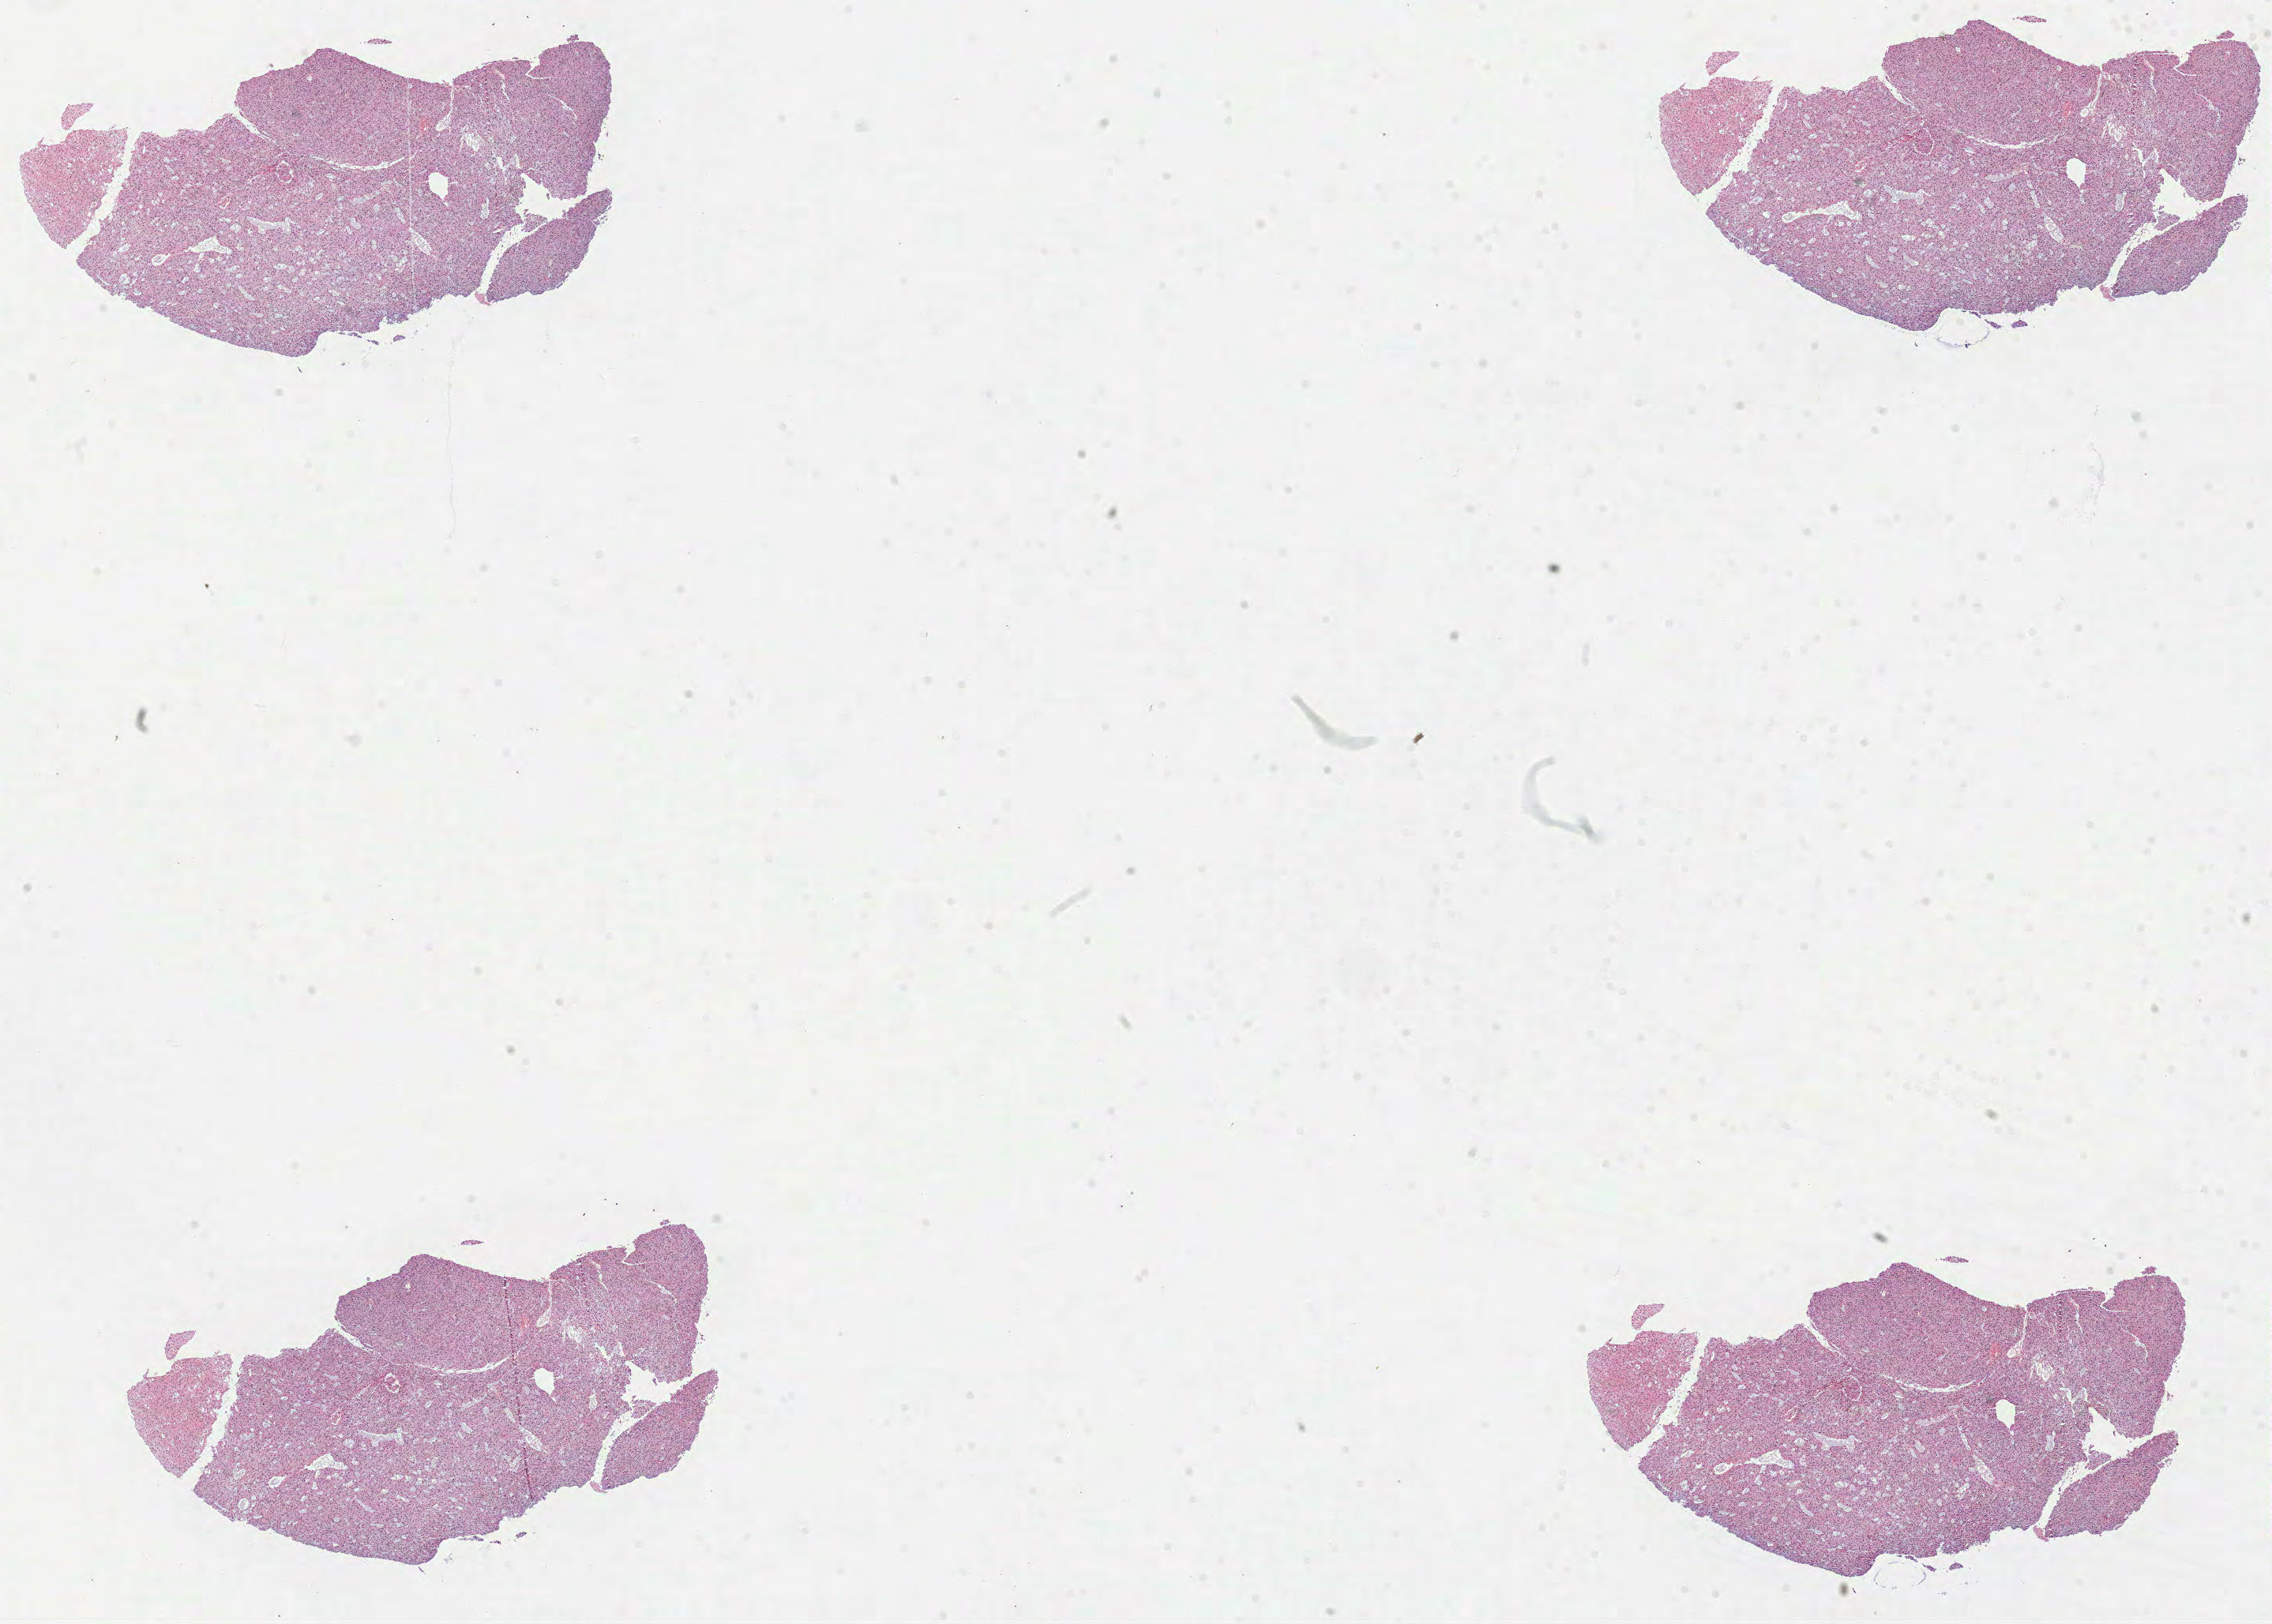
H&E whole-slide image, low-resolution overview of the scanned area, about 23.2 x 16.6 mm; FFPE section; primary tumour sample from the brain. Patient: male, age at initial diagnosis 31 years. Histologic grade: G2 (moderately differentiated).
Diagnosis: Mixed glioma (cerebrum).